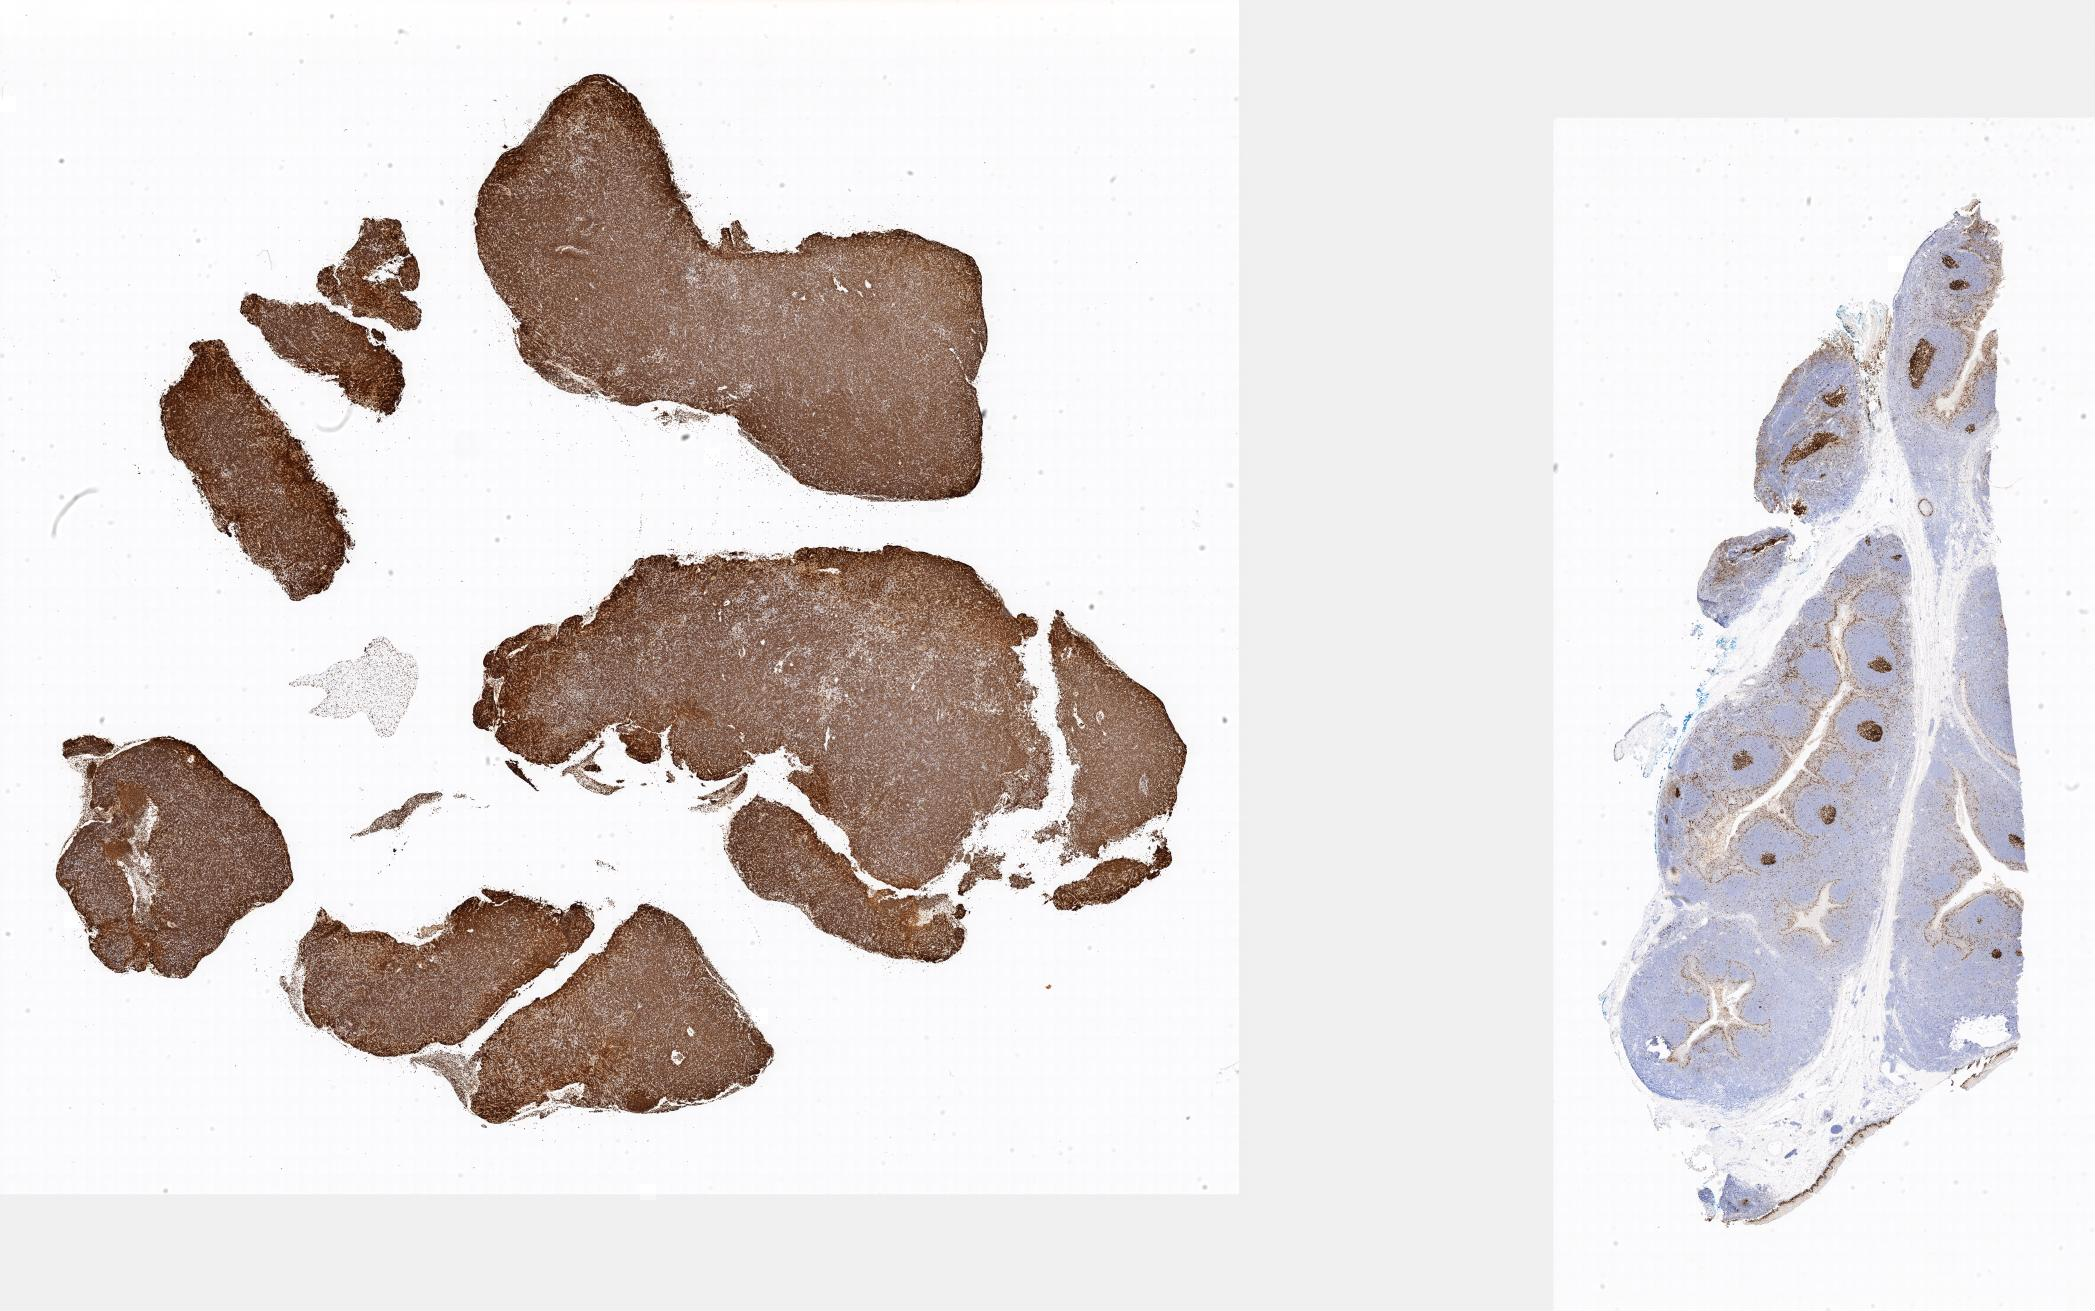
Immunohistochemistry (IHC) whole-slide image stained for Ki-67 — a low-resolution overview of the entire scanned area; specimen: tumor tissue; anatomic site: soft tissue. Patient: female, age at initial diagnosis 9 years.
- diagnosis: Burkitt lymphoma, NOS